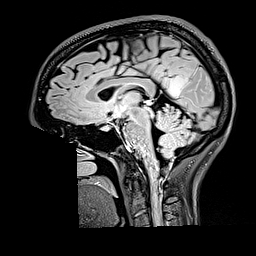
Brain MRI from a brain-tumour surgery series, one sagittal slice. Position 86 of 176 along the scan axis. T2 FLAIR. 1 mm slice thickness. 256 × 256 image matrix, field of view 256 × 256 mm. From the clinical record (not read from this slice): histopathology: Oligodendroglioma; WHO grade: 2; IDH mutation: yes.
Annotated regions visible in this slice (outlined manually by an expert reader):
- tumour: box from (x=168, y=73) to (x=189, y=96) px